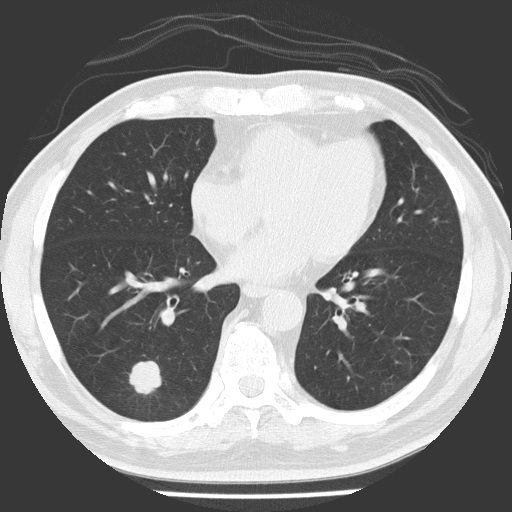
Low-dose screening chest CT, one axial slice; slice 66 of 154 in the series (ordered by position); reconstruction kernel FC51; lung window (W 1500 / L -600 HU); 2 mm slice thickness; 512 × 512 image matrix.
Annotated regions visible in this slice (manually delineated by an expert):
- lesion 1 (tumor, lower lobe of right lung): bounding box [x1, y1, x2, y2] px = [129, 361, 161, 395]